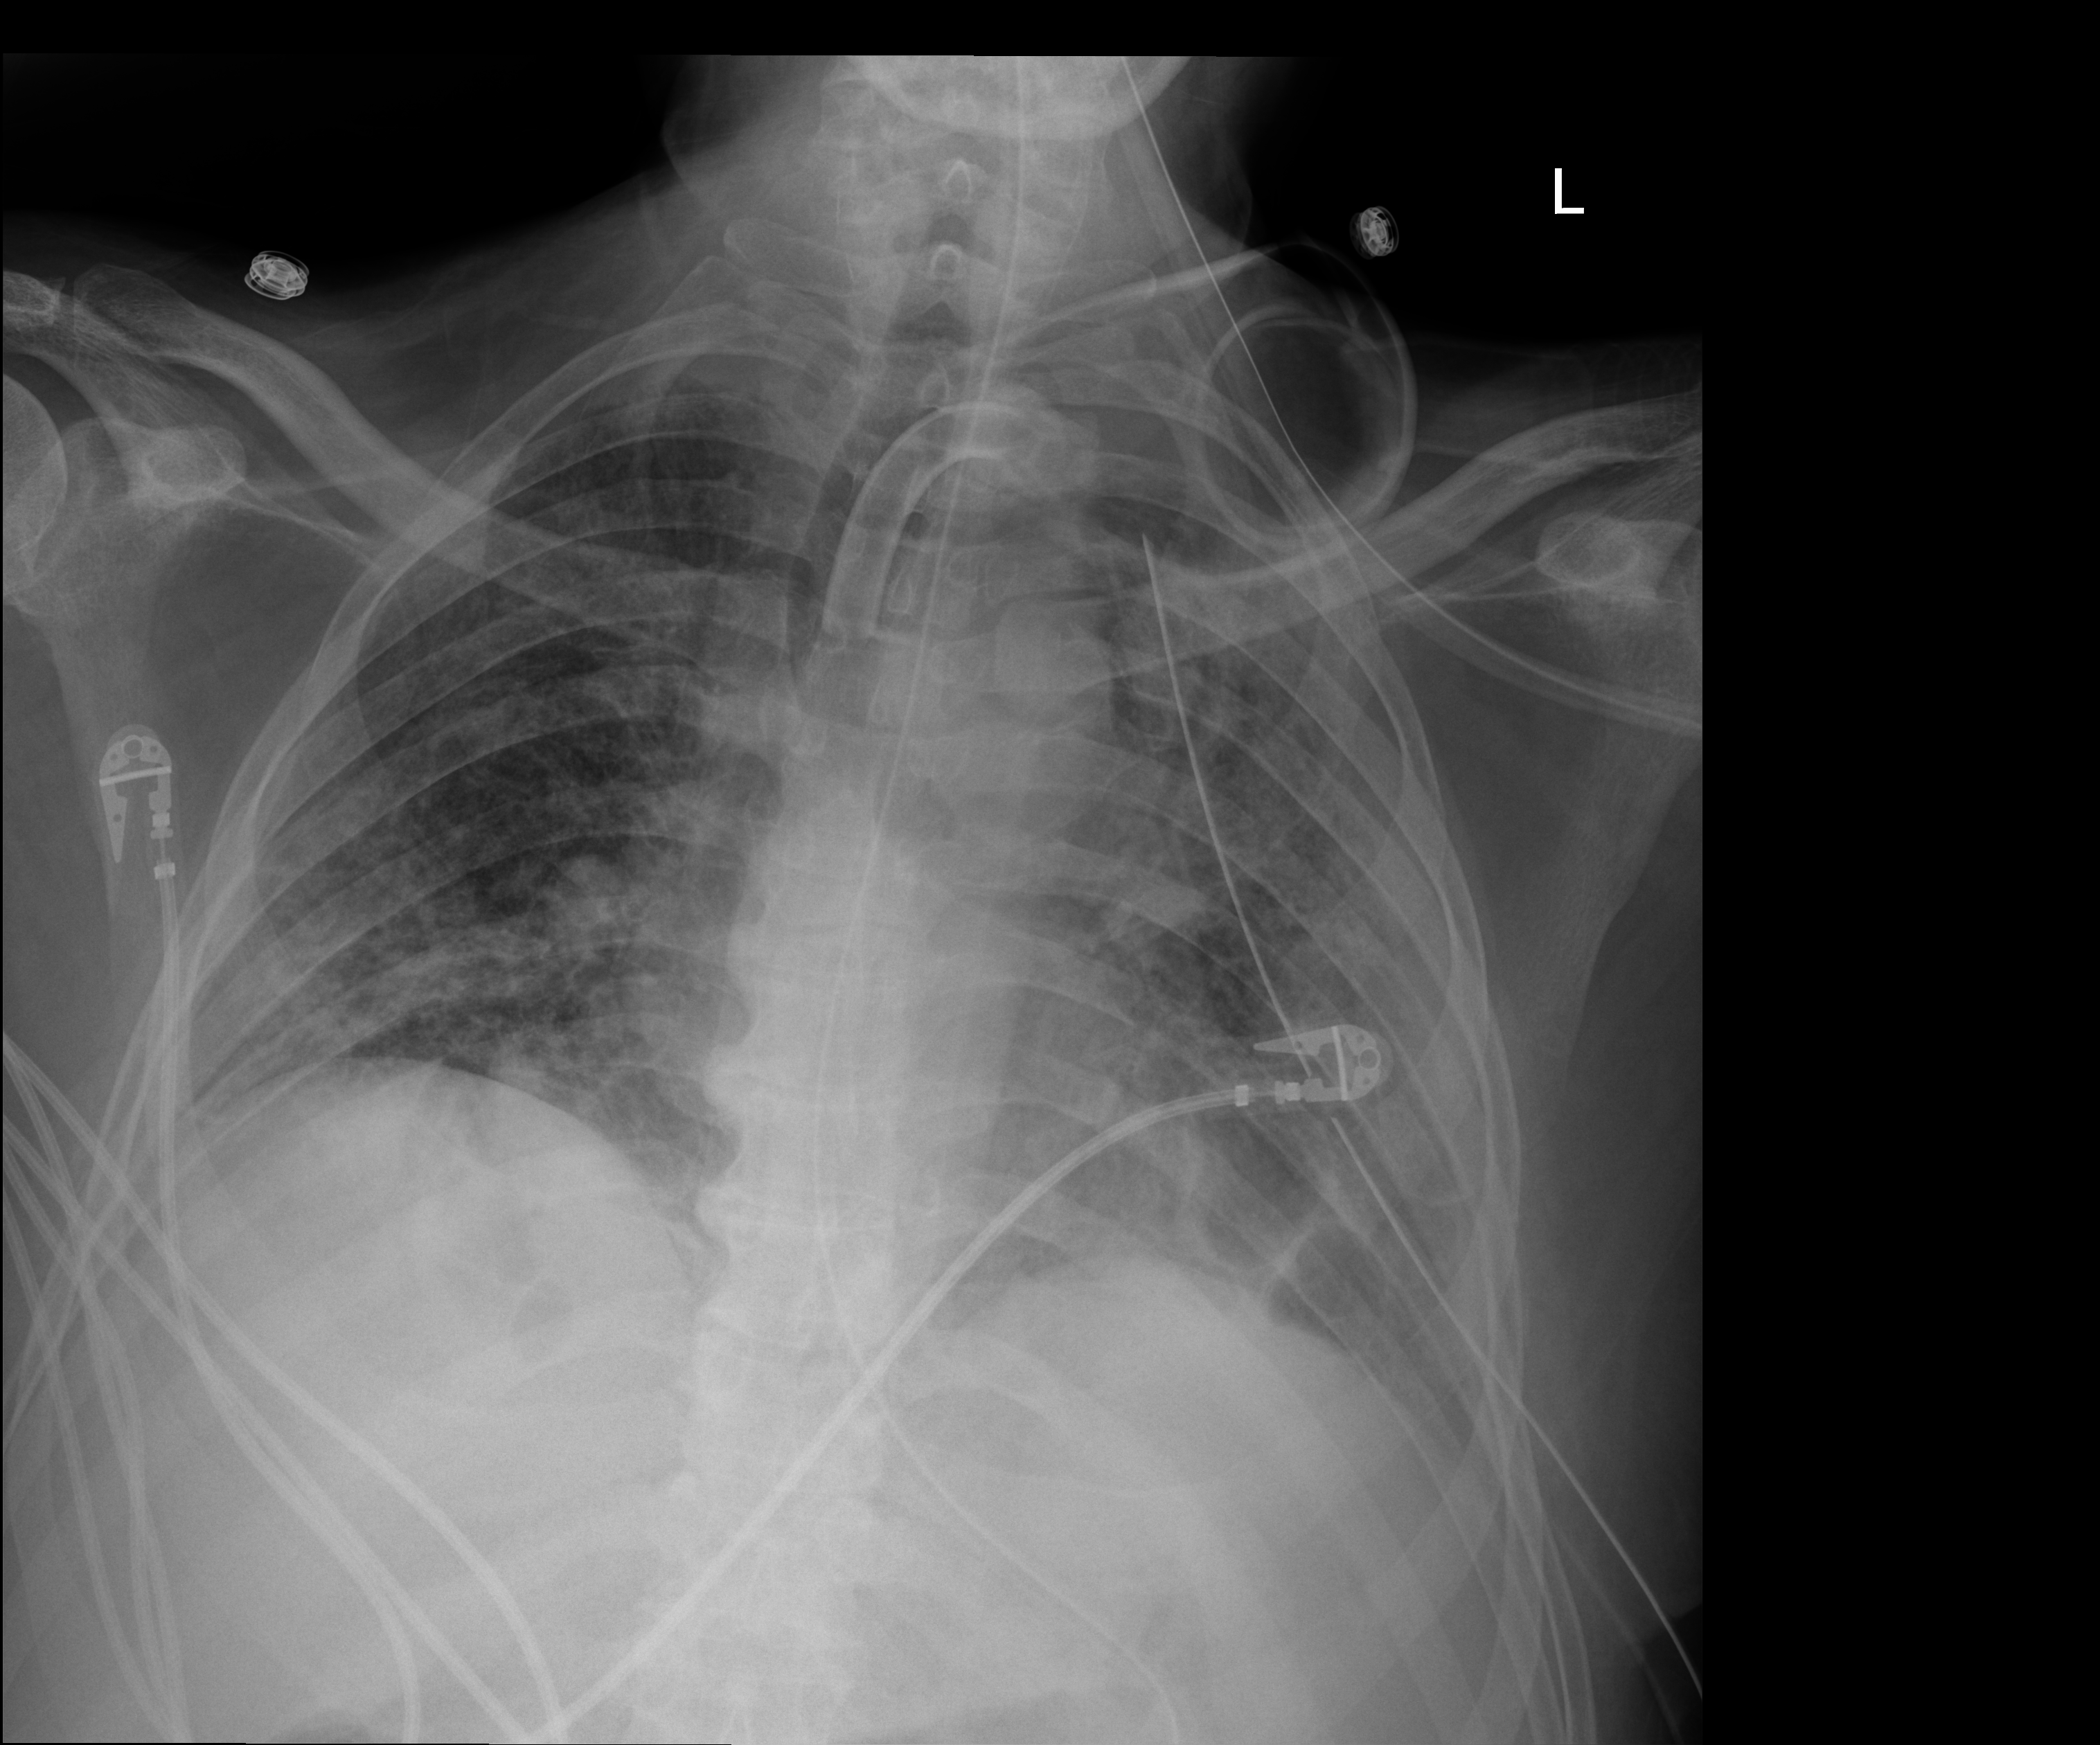
Bedside chest radiograph (digital radiography). Male patient hospitalised with COVID-19, age 18–59 years.
From the hospital-stay record, not from the radiograph (when in the stay this image was taken is not recorded): mechanically ventilated during this hospital stay: yes; admitted to intensive care during this hospital stay: yes.